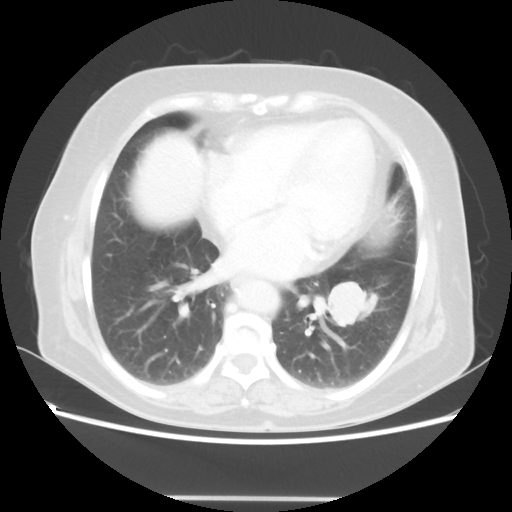
Chest CT, one axial slice; position 23 of 56 along the scan axis; reconstruction kernel STANDARD; lung window (W 1500 / L -600 HU); 5 mm slice thickness; 512 × 512 image matrix. Female patient, age 73 years. From the clinical record (not read from this slice): clinical TNM (as recorded): T1c N0 M0.
Outlined on this slice (bounding box drawn by a radiologist):
- lung tumour (recorded histology: adenocarcinoma): box from (x=325, y=274) to (x=384, y=332) px